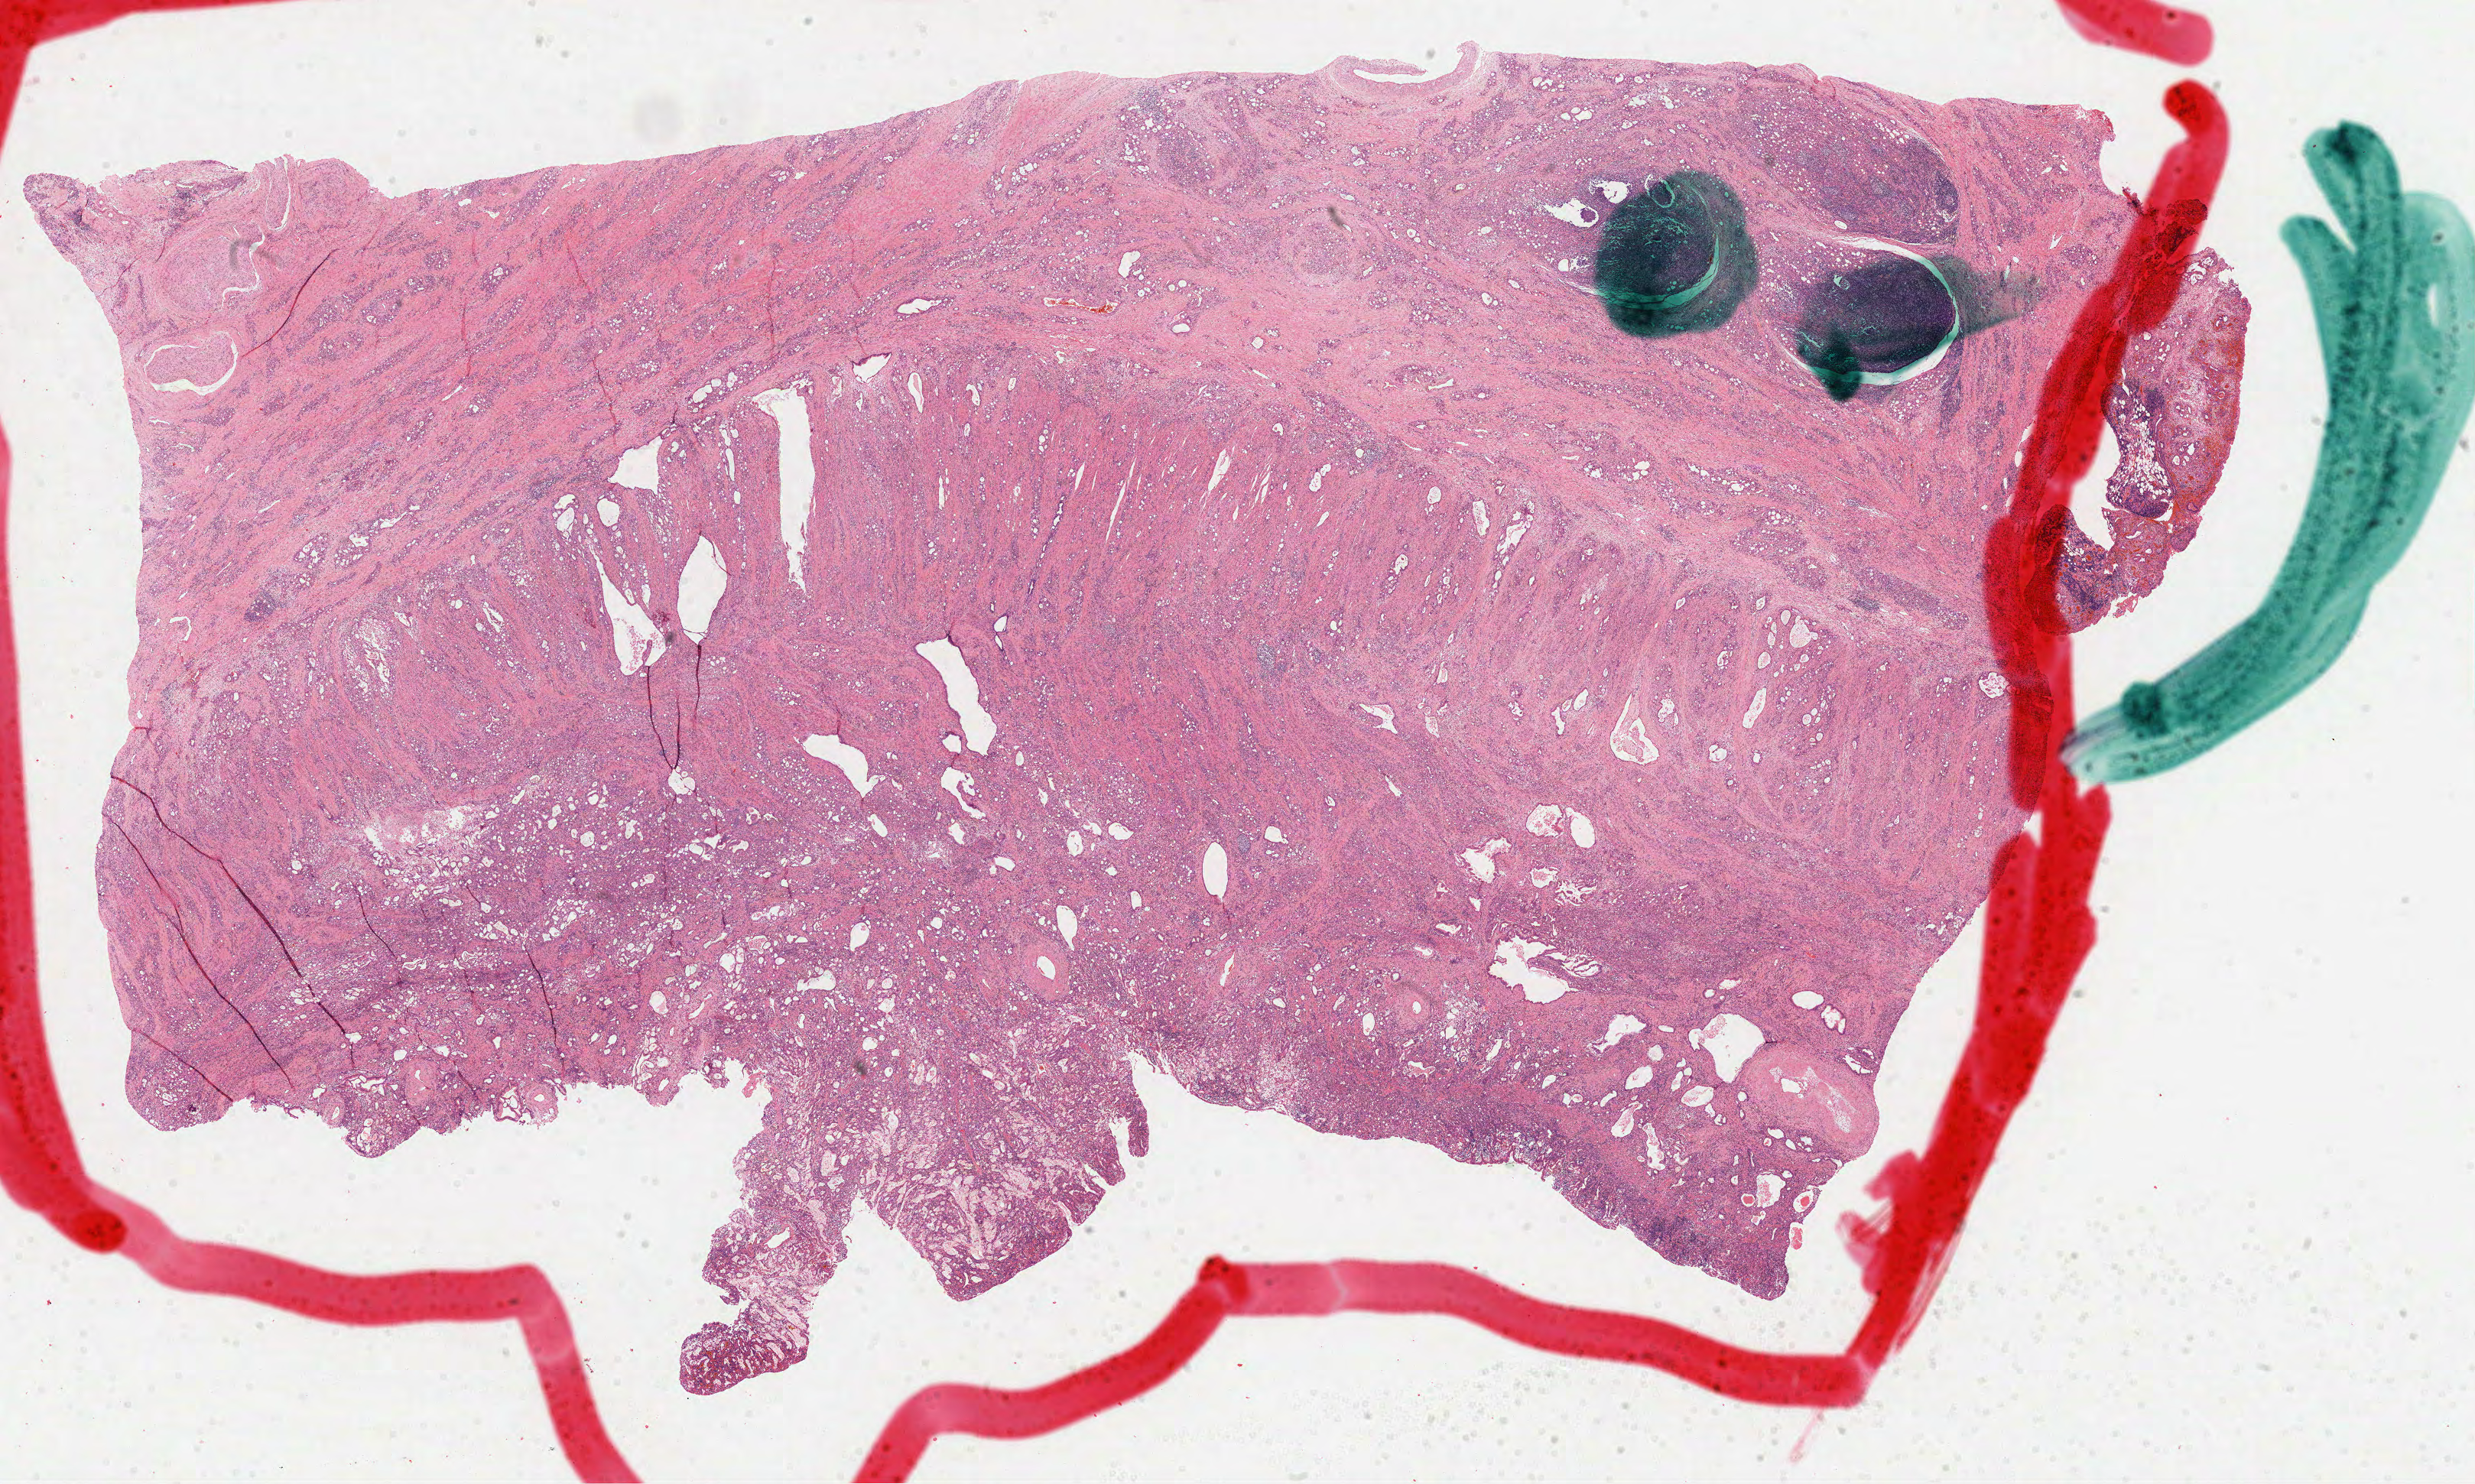
Hematoxylin and eosin (H&E) stained whole-slide image — shown as a low-resolution overview of the whole scanned area (about 26.1 x 15.7 mm). Formalin-fixed paraffin-embedded (FFPE) diagnostic section. Sample: primary tumour, stomach. Male patient; age at initial diagnosis 62 years. Histologic grade: G3 (poorly differentiated).
Pathologic diagnosis: Adenocarcinoma, NOS (cardia, NOS). Lymph nodes positive (case pathology): 5 of 15 examined. AJCC pathologic stage: IIB.